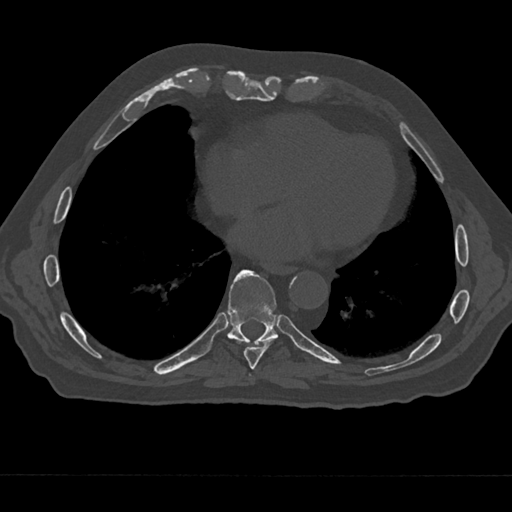
CT including the spine, one axial slice. Reconstruction kernel Br40s/3. 120 kVp. Bone window (W 1800 / L 400 HU). 0.5 mm slice thickness. 512 × 512 image matrix, field of view 377 × 377 mm. Male patient, age 75 years. Case-level facts recorded for this patient, not image findings: primary cancer: renal; vertebrae with lytic lesions (as recorded): T4.
Annotated regions visible in this slice (semi-automatically segmented with operator editing):
- T7 vertebra: box from (x=248, y=373) to (x=255, y=383) px
- T8 vertebra: (x=237, y=338)–(x=276, y=369)
- T9 vertebra: (x=226, y=269)–(x=283, y=344)